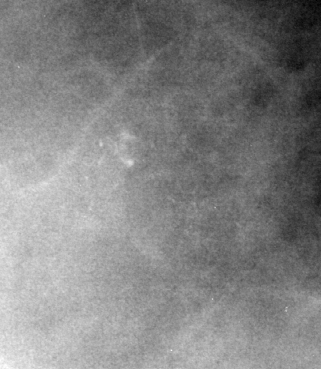
Crop from a digitized film mammogram around one marked abnormality, right breast, MLO view, BI-RADS breast density category 3 (scale 1–4).
Calcifications, morphology amorphous, distribution clustered; BI-RADS assessment category 4; pathology (as recorded): benign.